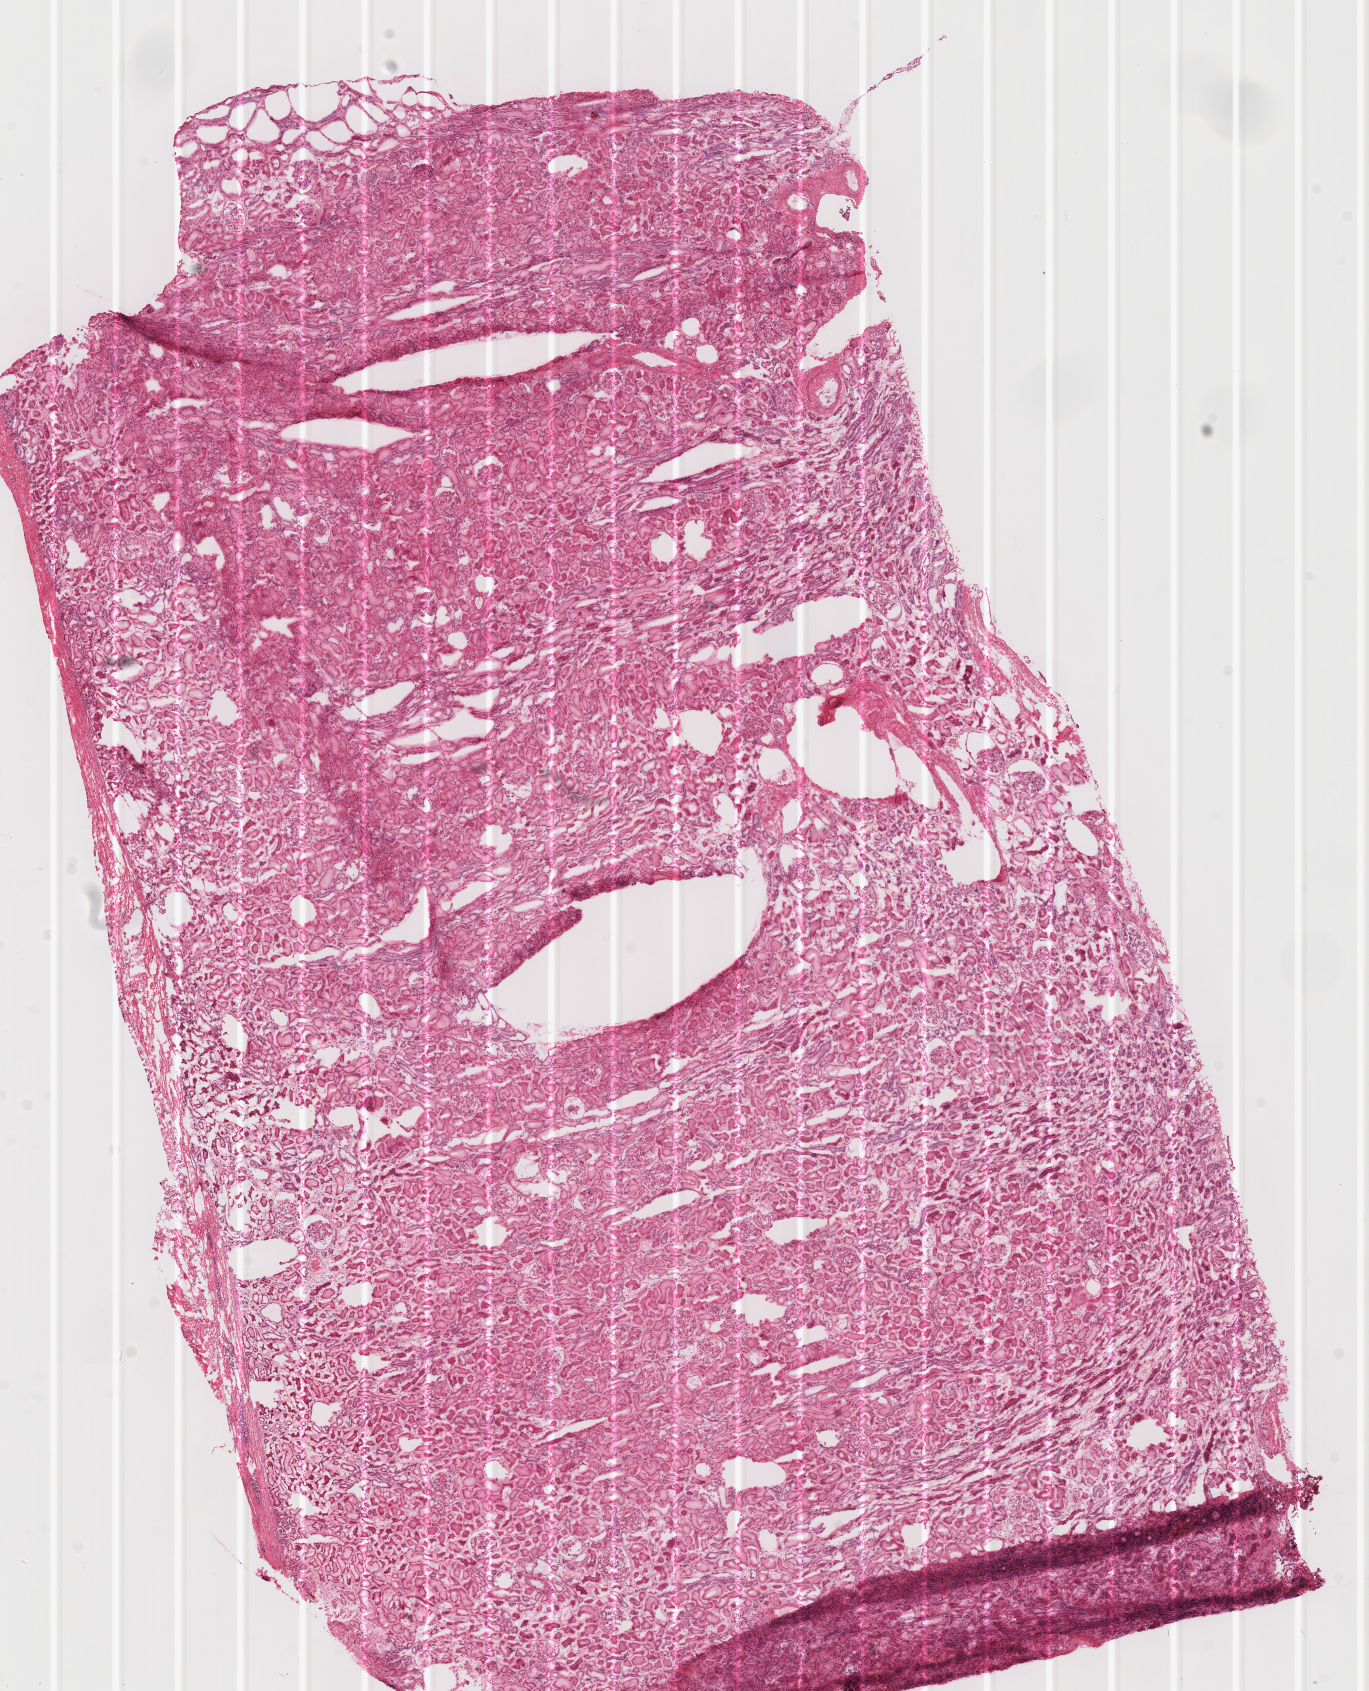
Digitized H&E-stained tissue section (whole slide) — a low-resolution overview of the entire scanned area, about 10.8 x 13.3 mm (from a 40x scan); frozen section from the top of the tissue portion; solid tissue normal (non-tumour tissue) sample from the kidney. Male patient; age at initial diagnosis 55 years. Infiltration values recorded for this section: lymphocyte infiltration 1%, monocyte infiltration 0%, neutrophil infiltration 0%.
- this section: solid tissue normal sample (biorepository sample class)
- patient diagnosis: Renal cell carcinoma, chromophobe type